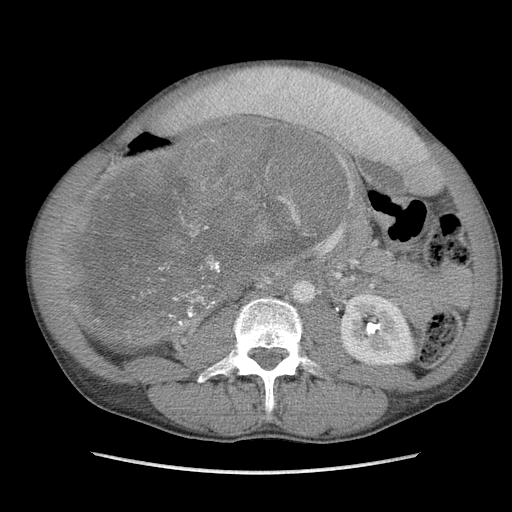
Contrast-enhanced abdominal CT, one axial slice. Slice 49 of 115 in the series (ordered by position). Soft-tissue window (W 400 / L 40 HU). 5 mm slice thickness. 512 × 512 image matrix. Male patient. From the clinical record (not read from this slice): diagnosis: adrenocortical carcinoma; tumour side: right adrenal; Ki-67 index: 13 %; stage (as recorded): 3.
Outlined on this slice (semi-automatic segmentation, software-assisted and operator-edited):
- mass: bounding box <68,119,341,344> (left, top, right, bottom; pixels)